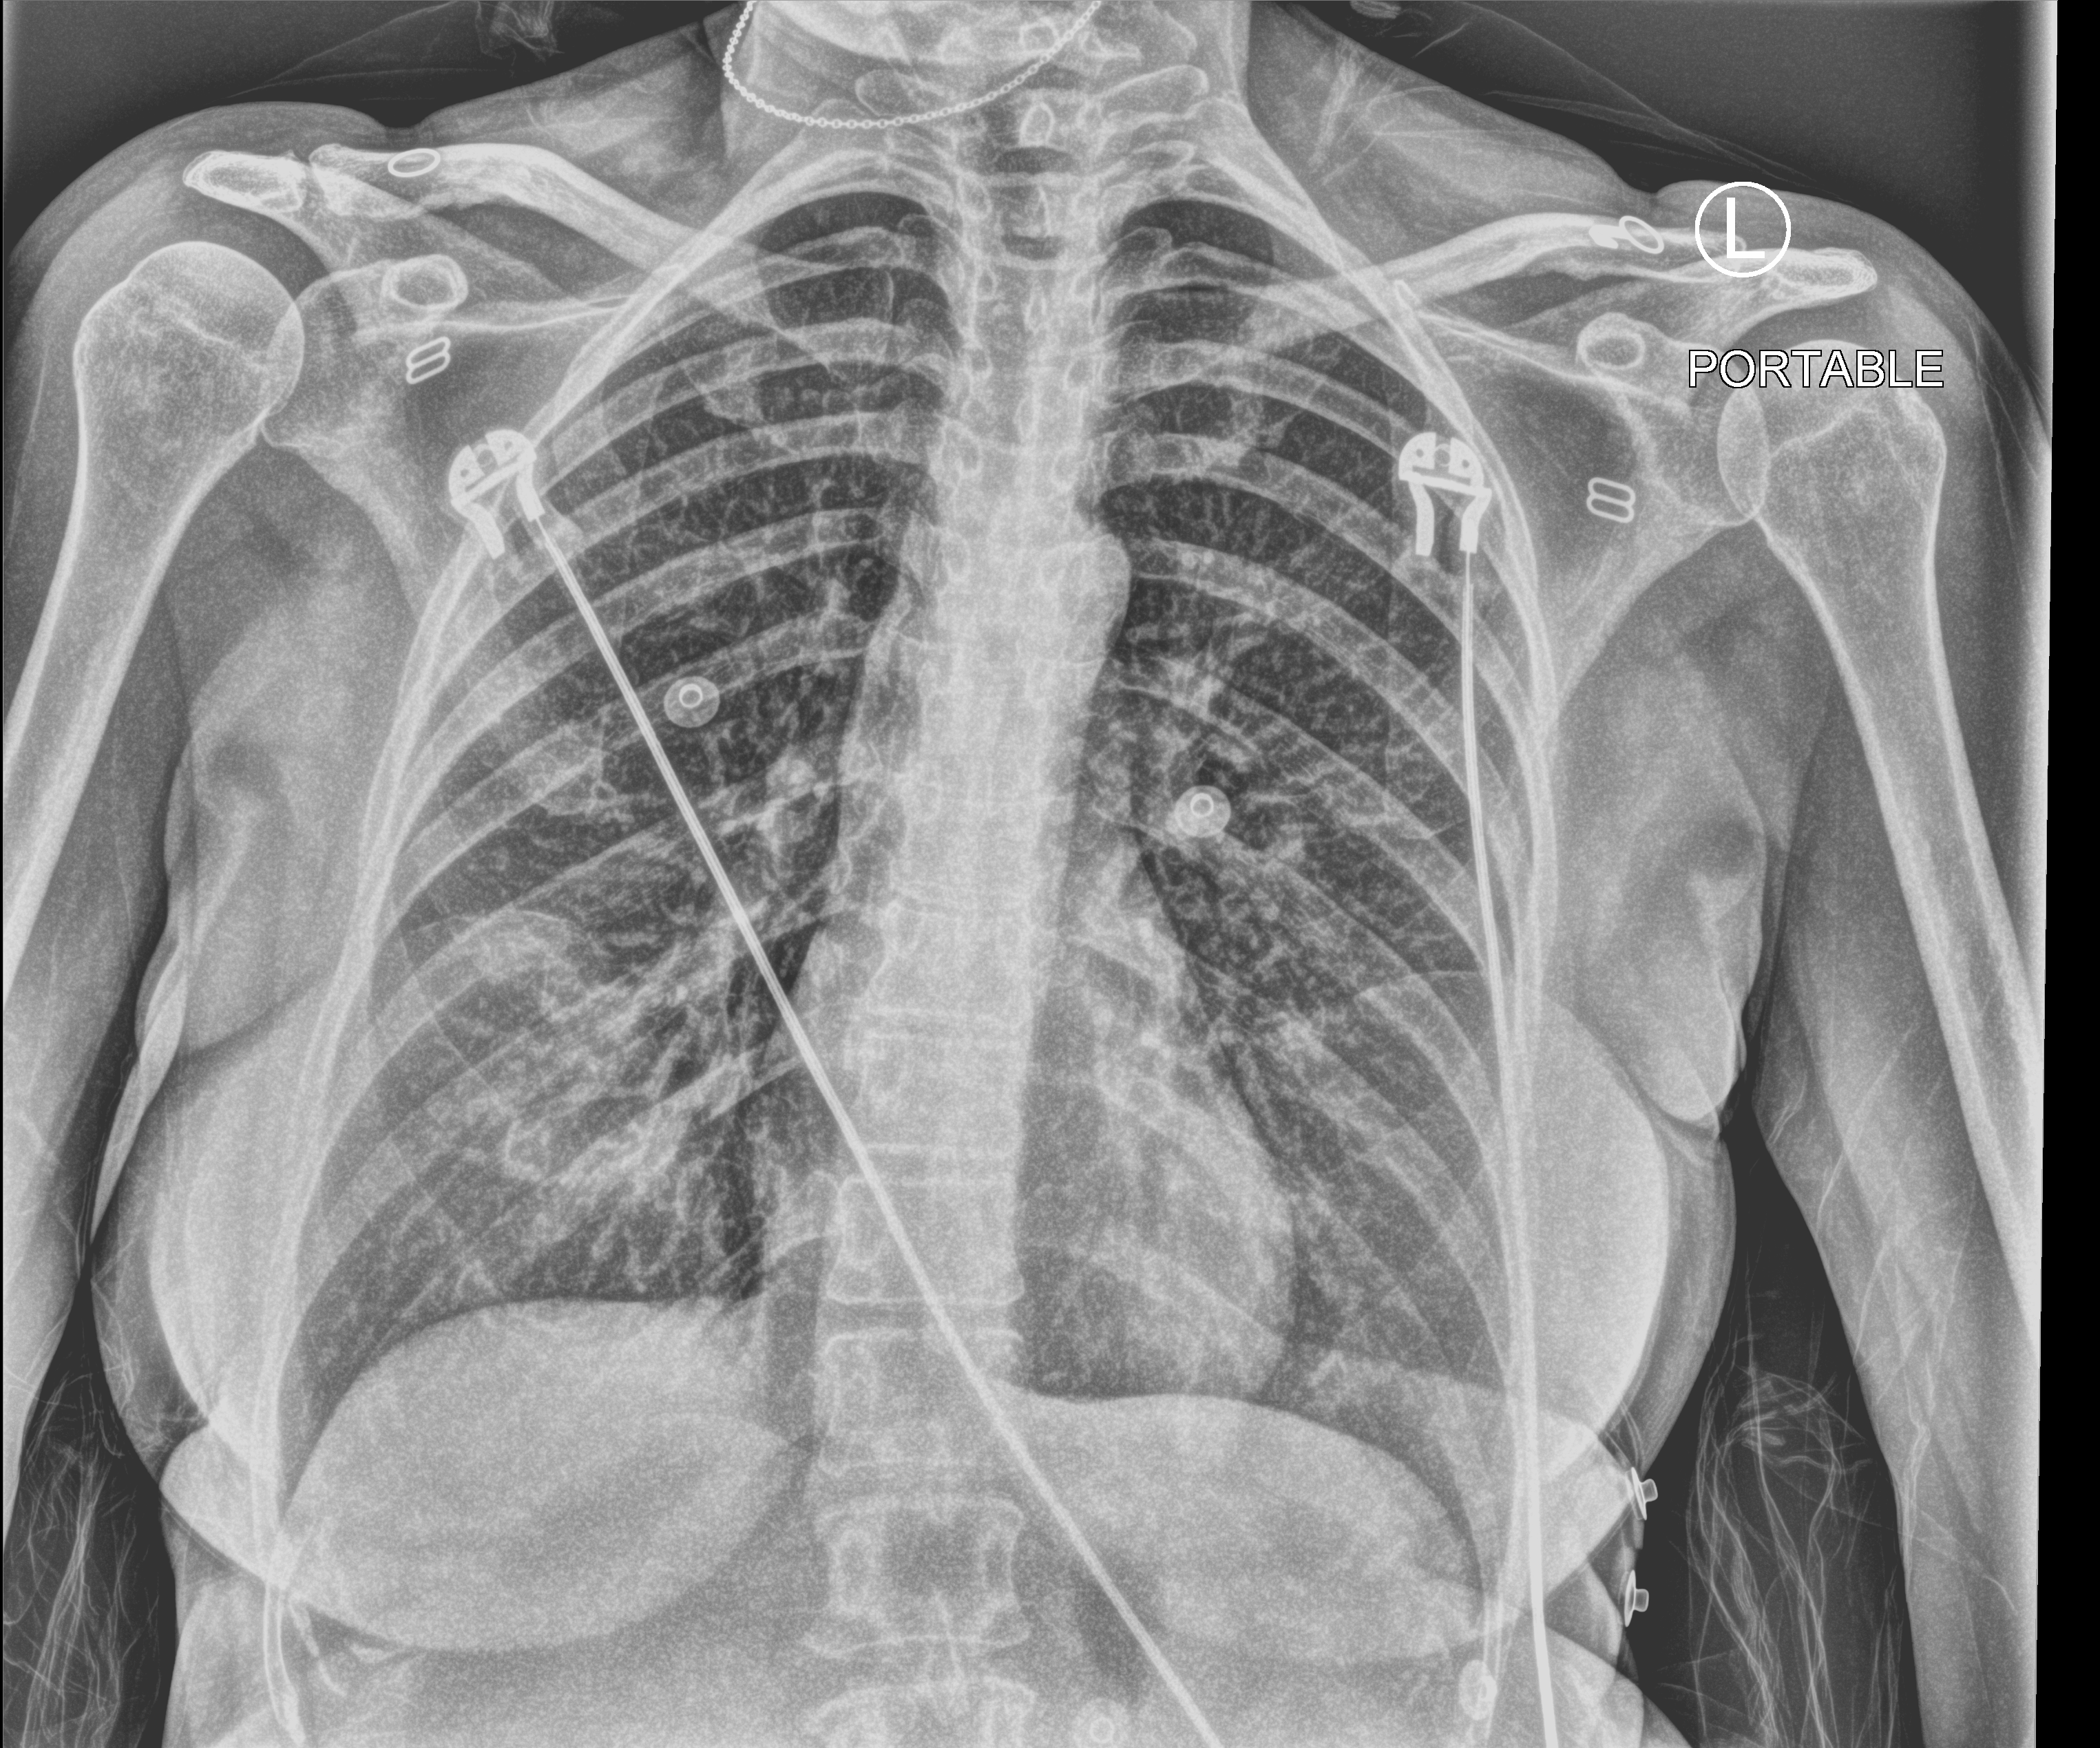
Bedside chest radiograph (computed radiography); anteroposterior (AP) projection. Patient hospitalised with COVID-19; female, aged 18–59 years.
From the hospital-stay record, not from the radiograph (when in the stay this image was taken is not recorded): admitted to intensive care during this hospital stay: no; mechanically ventilated during this hospital stay: no.